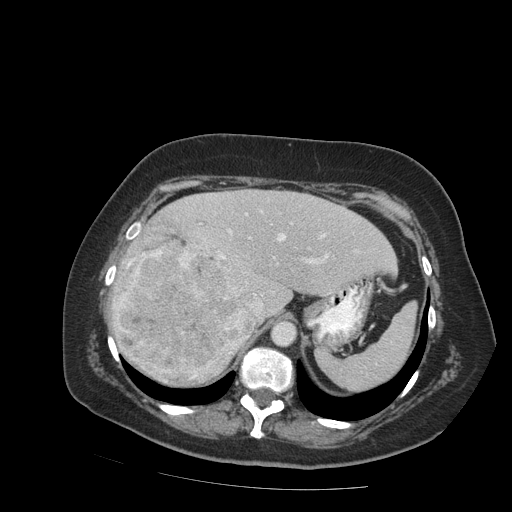
Contrast-enhanced abdominal CT (liver protocol), one axial slice; reconstruction kernel STANDARD; 140 kVp; soft-tissue window (W 400 / L 40 HU); 2.5 mm slice thickness; 512 × 512 image matrix, field of view 400 × 400 mm. From the clinical record (not read from this slice): diagnosis: hepatocellular carcinoma (patient treated with transarterial chemoembolisation; whether this scan precedes or follows treatment is not stated here); TNM stage (as recorded): Stage-IVB; Child-Pugh class: A; tumour differentiation: moderately differentiated; tumour nodularity: uninodular.
Annotated regions visible in this slice (semi-automatically segmented with operator editing):
- abdominal aorta: bounding box [x1, y1, x2, y2] px = [272, 322, 295, 346]
- liver parenchyma outside the tumour (the mass and vessels are separate outlines, so this box may not span the whole liver): [110, 190, 396, 344]
- mass: [114, 225, 253, 386]
- liver vessels: [131, 211, 328, 308]